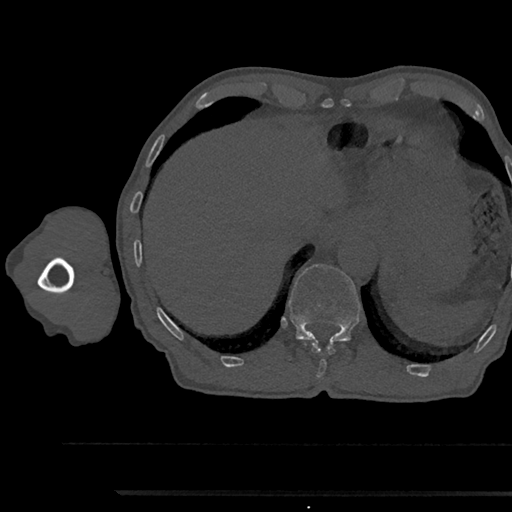
CT including the spine, one axial slice; slice 747 of 797 in the series (ordered by position); 120 kVp; bone window (W 1800 / L 400 HU); 512 × 512 image matrix, field of view 367 × 367 mm. Patient: male, 79 years. Case-level facts recorded for this patient, not image findings: primary cancer: prostate.
Structures marked on this image (semi-automatically segmented with operator editing):
- T11 vertebra: bounding box <313,341,334,378> (left, top, right, bottom; pixels)
- T12 vertebra: <288,264,360,343>